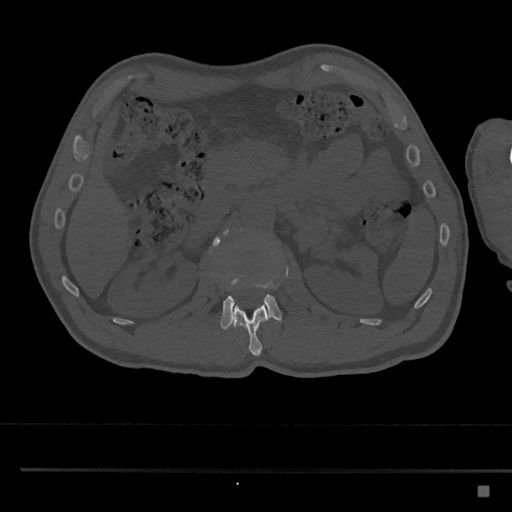
CT including the spine, one axial slice. Bone window (W 1800 / L 400 HU). 512 × 512 image matrix, field of view 391 × 391 mm. Male patient, age 59 years. From the clinical record (not read from this slice): primary cancer: prostate.
Annotated regions visible in this slice (semi-automatic segmentation, software-assisted and operator-edited):
- L1 vertebra: bounding box [x1, y1, x2, y2] px = [233, 302, 270, 356]
- L2 vertebra: [209, 229, 282, 330]